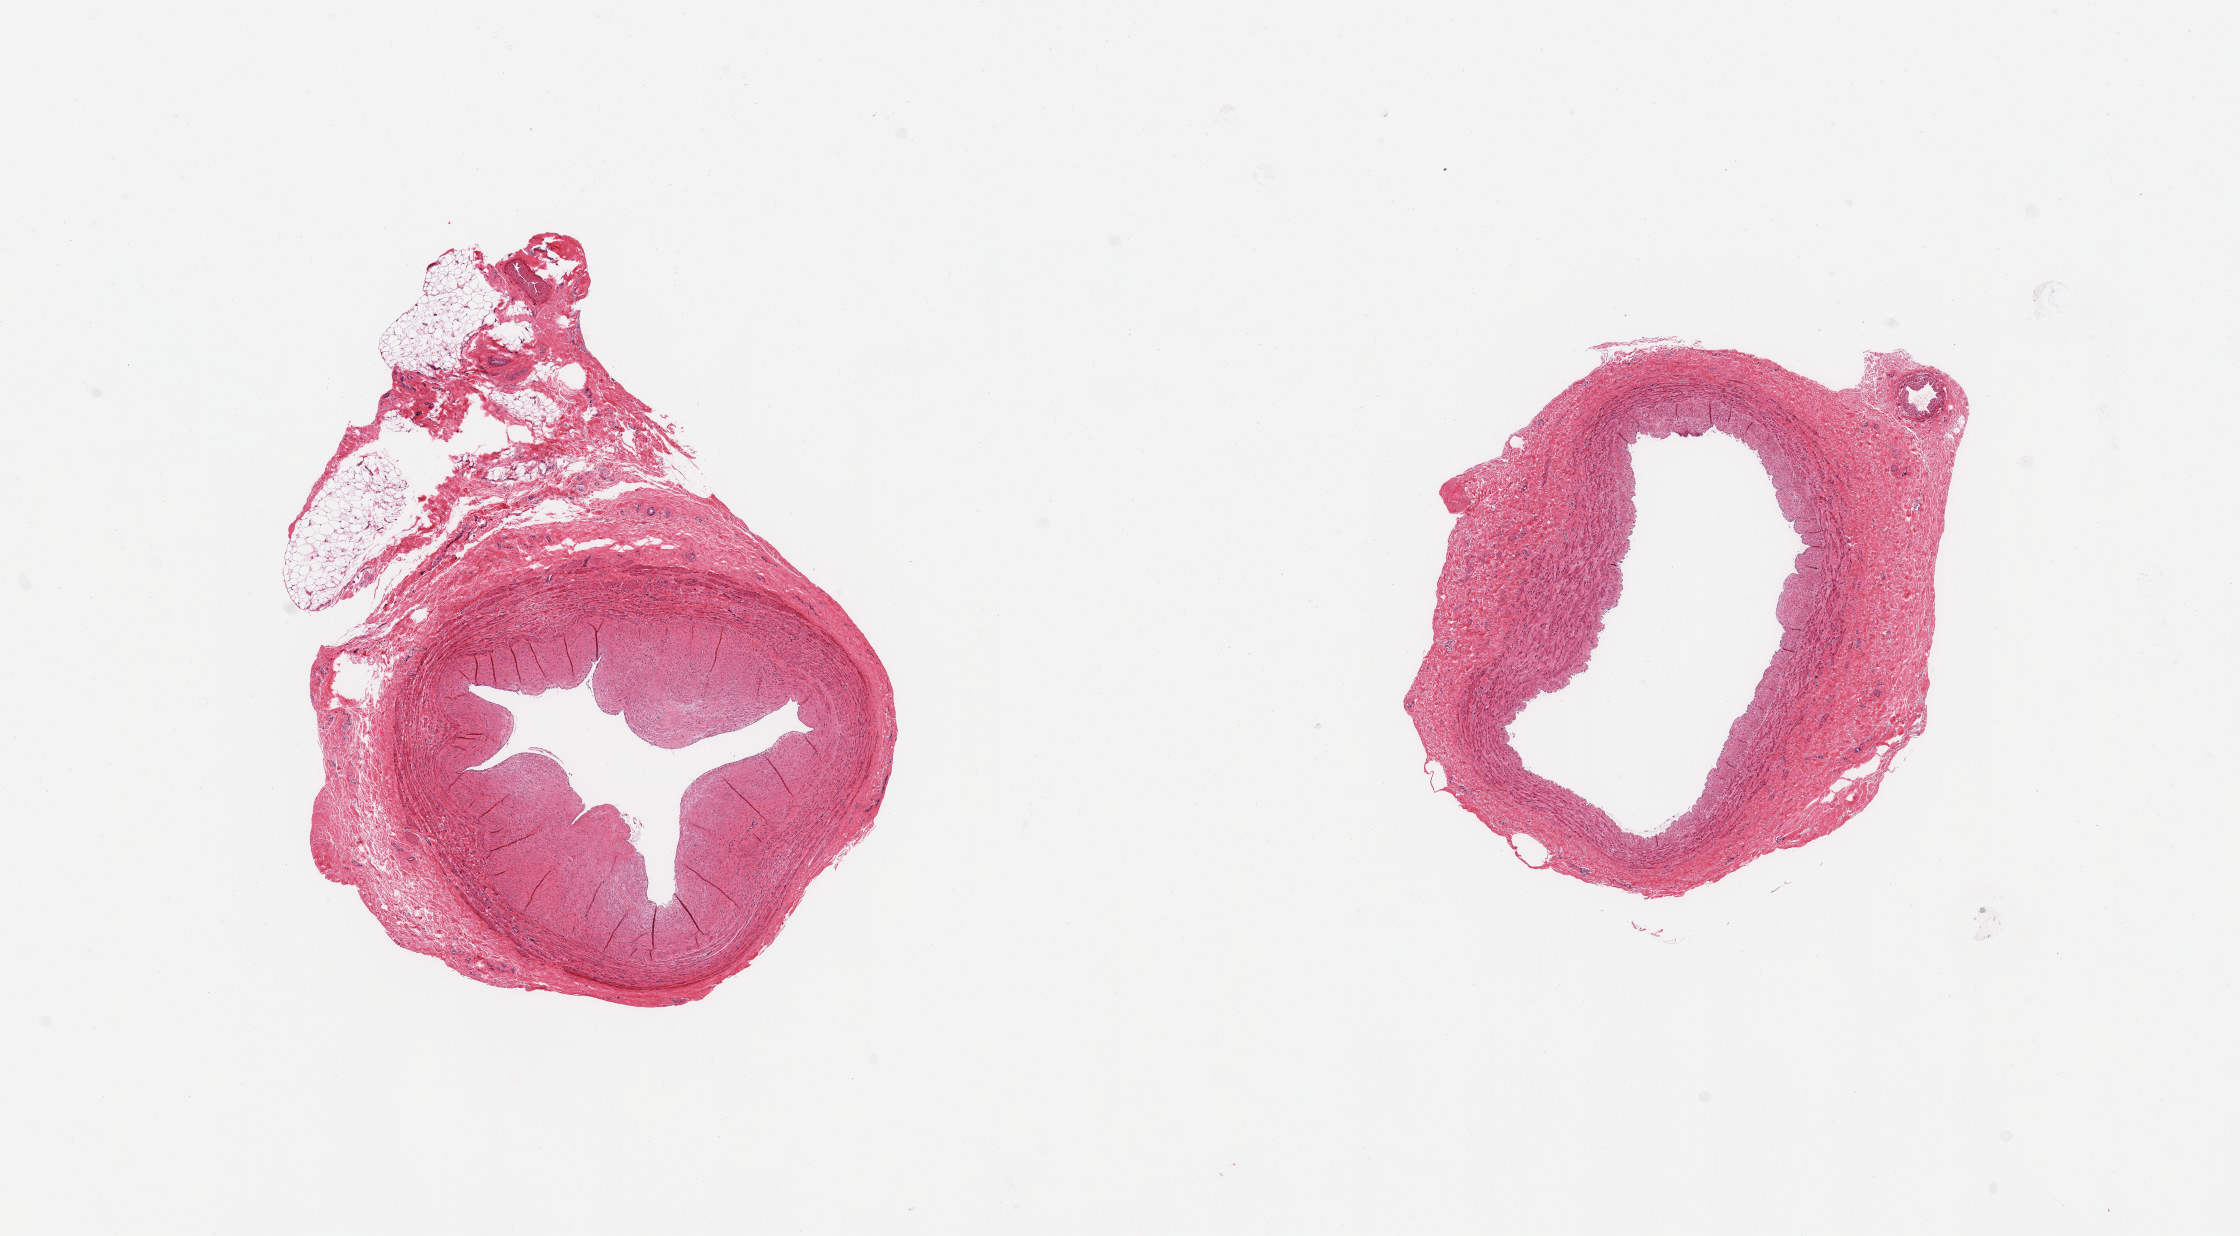
Whole-slide image, H&E stain — a low-resolution overview of the entire scanned area, about 17.7 x 9.8 mm, PAXgene-fixed, paraffin-embedded tissue, section of tibial artery (target tissue), tissue donor sample.
Pathologist's review note for this sample: 2 pieces; intimal thickening.